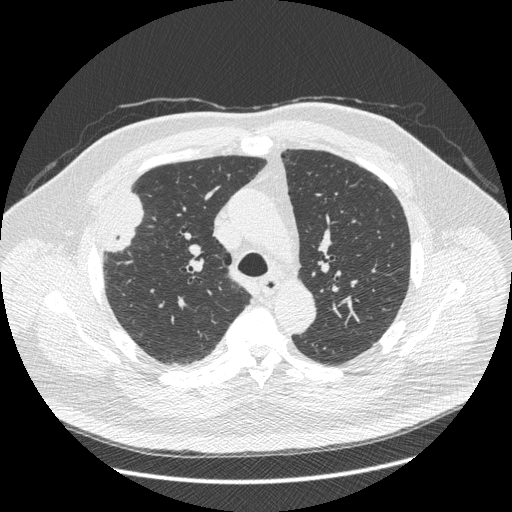
Low-dose screening chest CT, axial slice; third annual screen; lung window (W 1500 / L -600 HU); slice 131 of 426 in the series; 512 × 512 image matrix. Male participant, aged 66 years at enrolment.
• Lesion marked by an expert reader, bounding box <87,197,147,268> (left, top, right, bottom; pixels).
• Screening reader's record for this exam (one nodule recorded; not confirmed to be the boxed lesion): non-calcified nodule or mass ≥4 mm, right upper lobe, 48 × 25 mm, spiculated (stellate) margins, soft tissue attenuation, pre-existing on the prior screen: no.
• Lung cancer was diagnosed 35 days after this screen: non-small cell carcinoma, right upper lobe, stage IV (AJCC 6th edition), 50 mm at pathology.